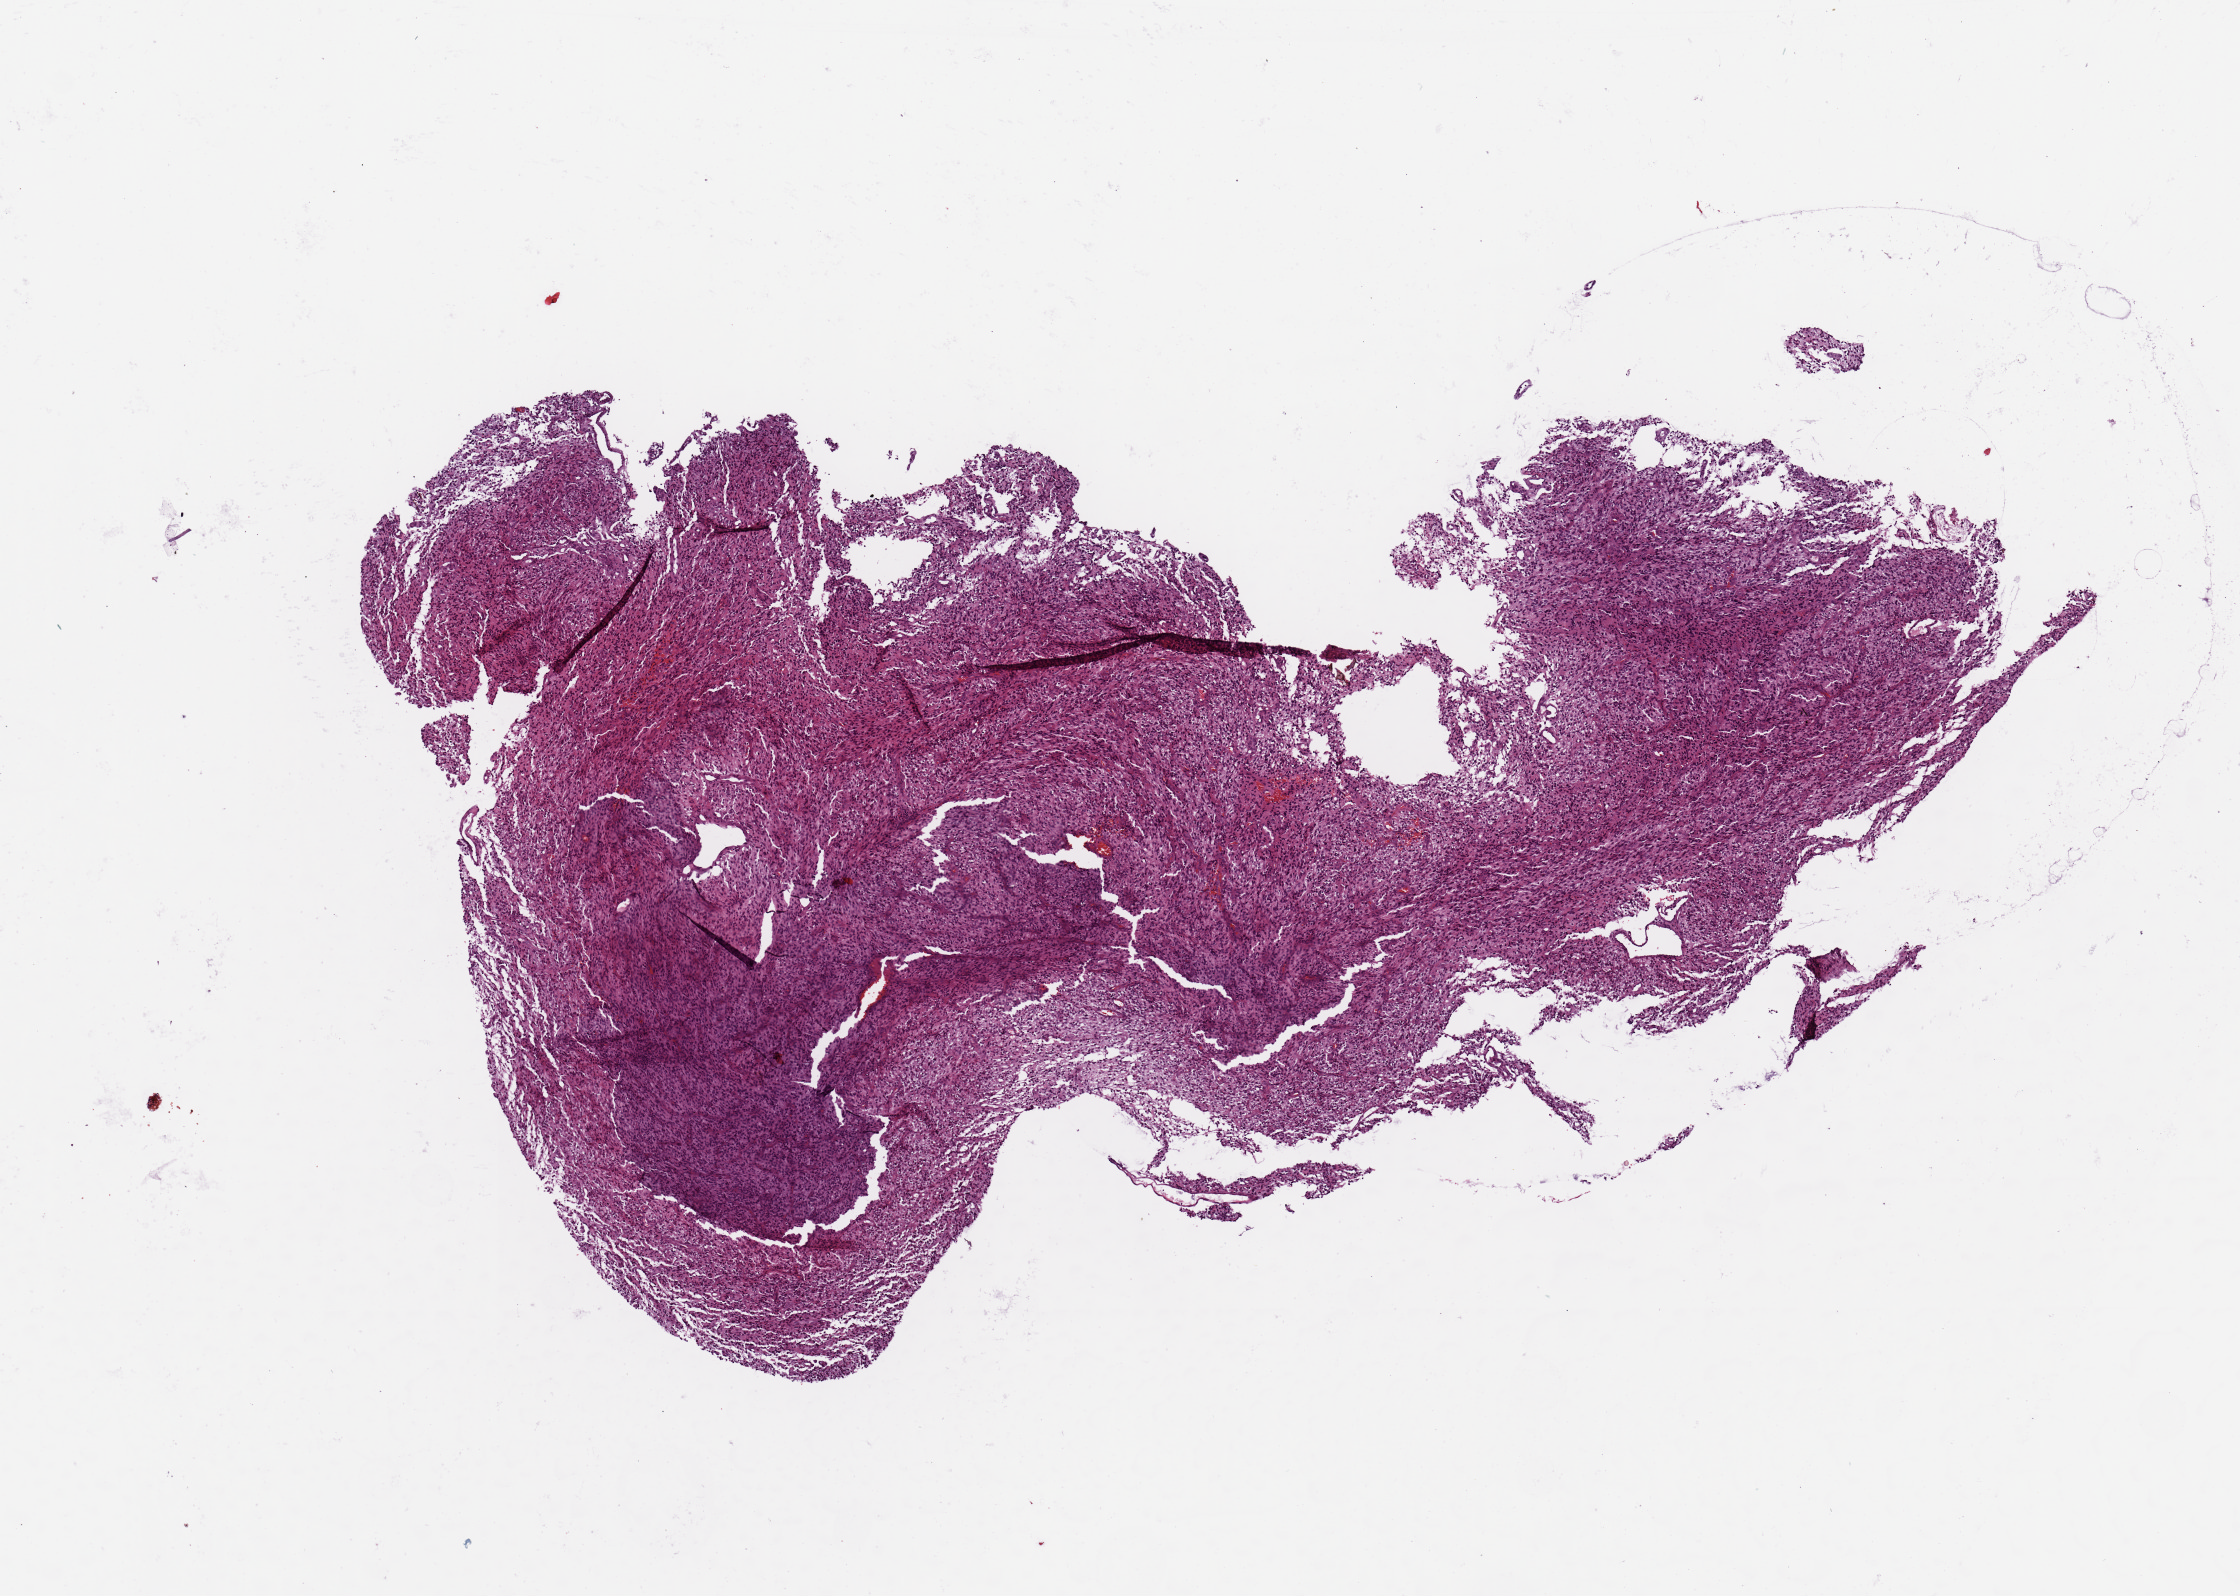
Whole-slide histology image, H&E-stained, a low-resolution overview of the entire scanned area, about 8.9 x 6.3 mm, tumour tissue sample, brain. Patient: male, age 54 years.
* histologic diagnosis: Glioblastoma